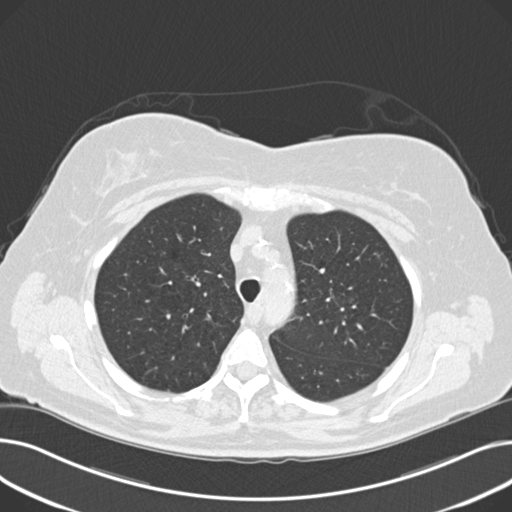
Low-dose screening chest CT, axial slice; third screening round (two years after baseline); lung window (W 1500 / L -600 HU); 2 mm slice thickness; standard (soft-tissue) reconstruction kernel (B30f); 120 kVp; slice 57 of 203 in the series. Female, age 60 years at enrolment. Current smoker at enrolment.
Lesion marked by an expert reader, bounding box [x1, y1, x2, y2] px = [358, 238, 411, 281]. The screening reader recorded 8 non-calcified nodules or masses ≥4 mm on this exam; which of them this box marks is not recorded. Later outcome: lung cancer diagnosed 176 days after this screen — non-small cell carcinoma, left upper lobe, poorly differentiated (G3), stage IB (AJCC 6th edition), 7 mm at pathology.